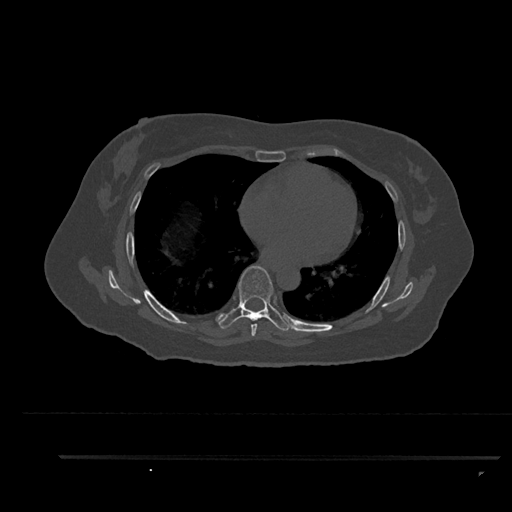
CT including the spine, one axial slice. Position 519 of 797 along the scan axis. 120 kVp. Bone window (W 1800 / L 400 HU). 0.5 mm slice thickness. 512 × 512 image matrix. Female patient, age 44 years. Case-level facts recorded for this patient, not image findings: primary cancer: renal.
Structures marked on this image (semi-automatic segmentation, software-assisted and operator-edited):
- T6 vertebra: bounding box <251,319,257,337> (left, top, right, bottom; pixels)
- T7 vertebra: <219,266,291,331>